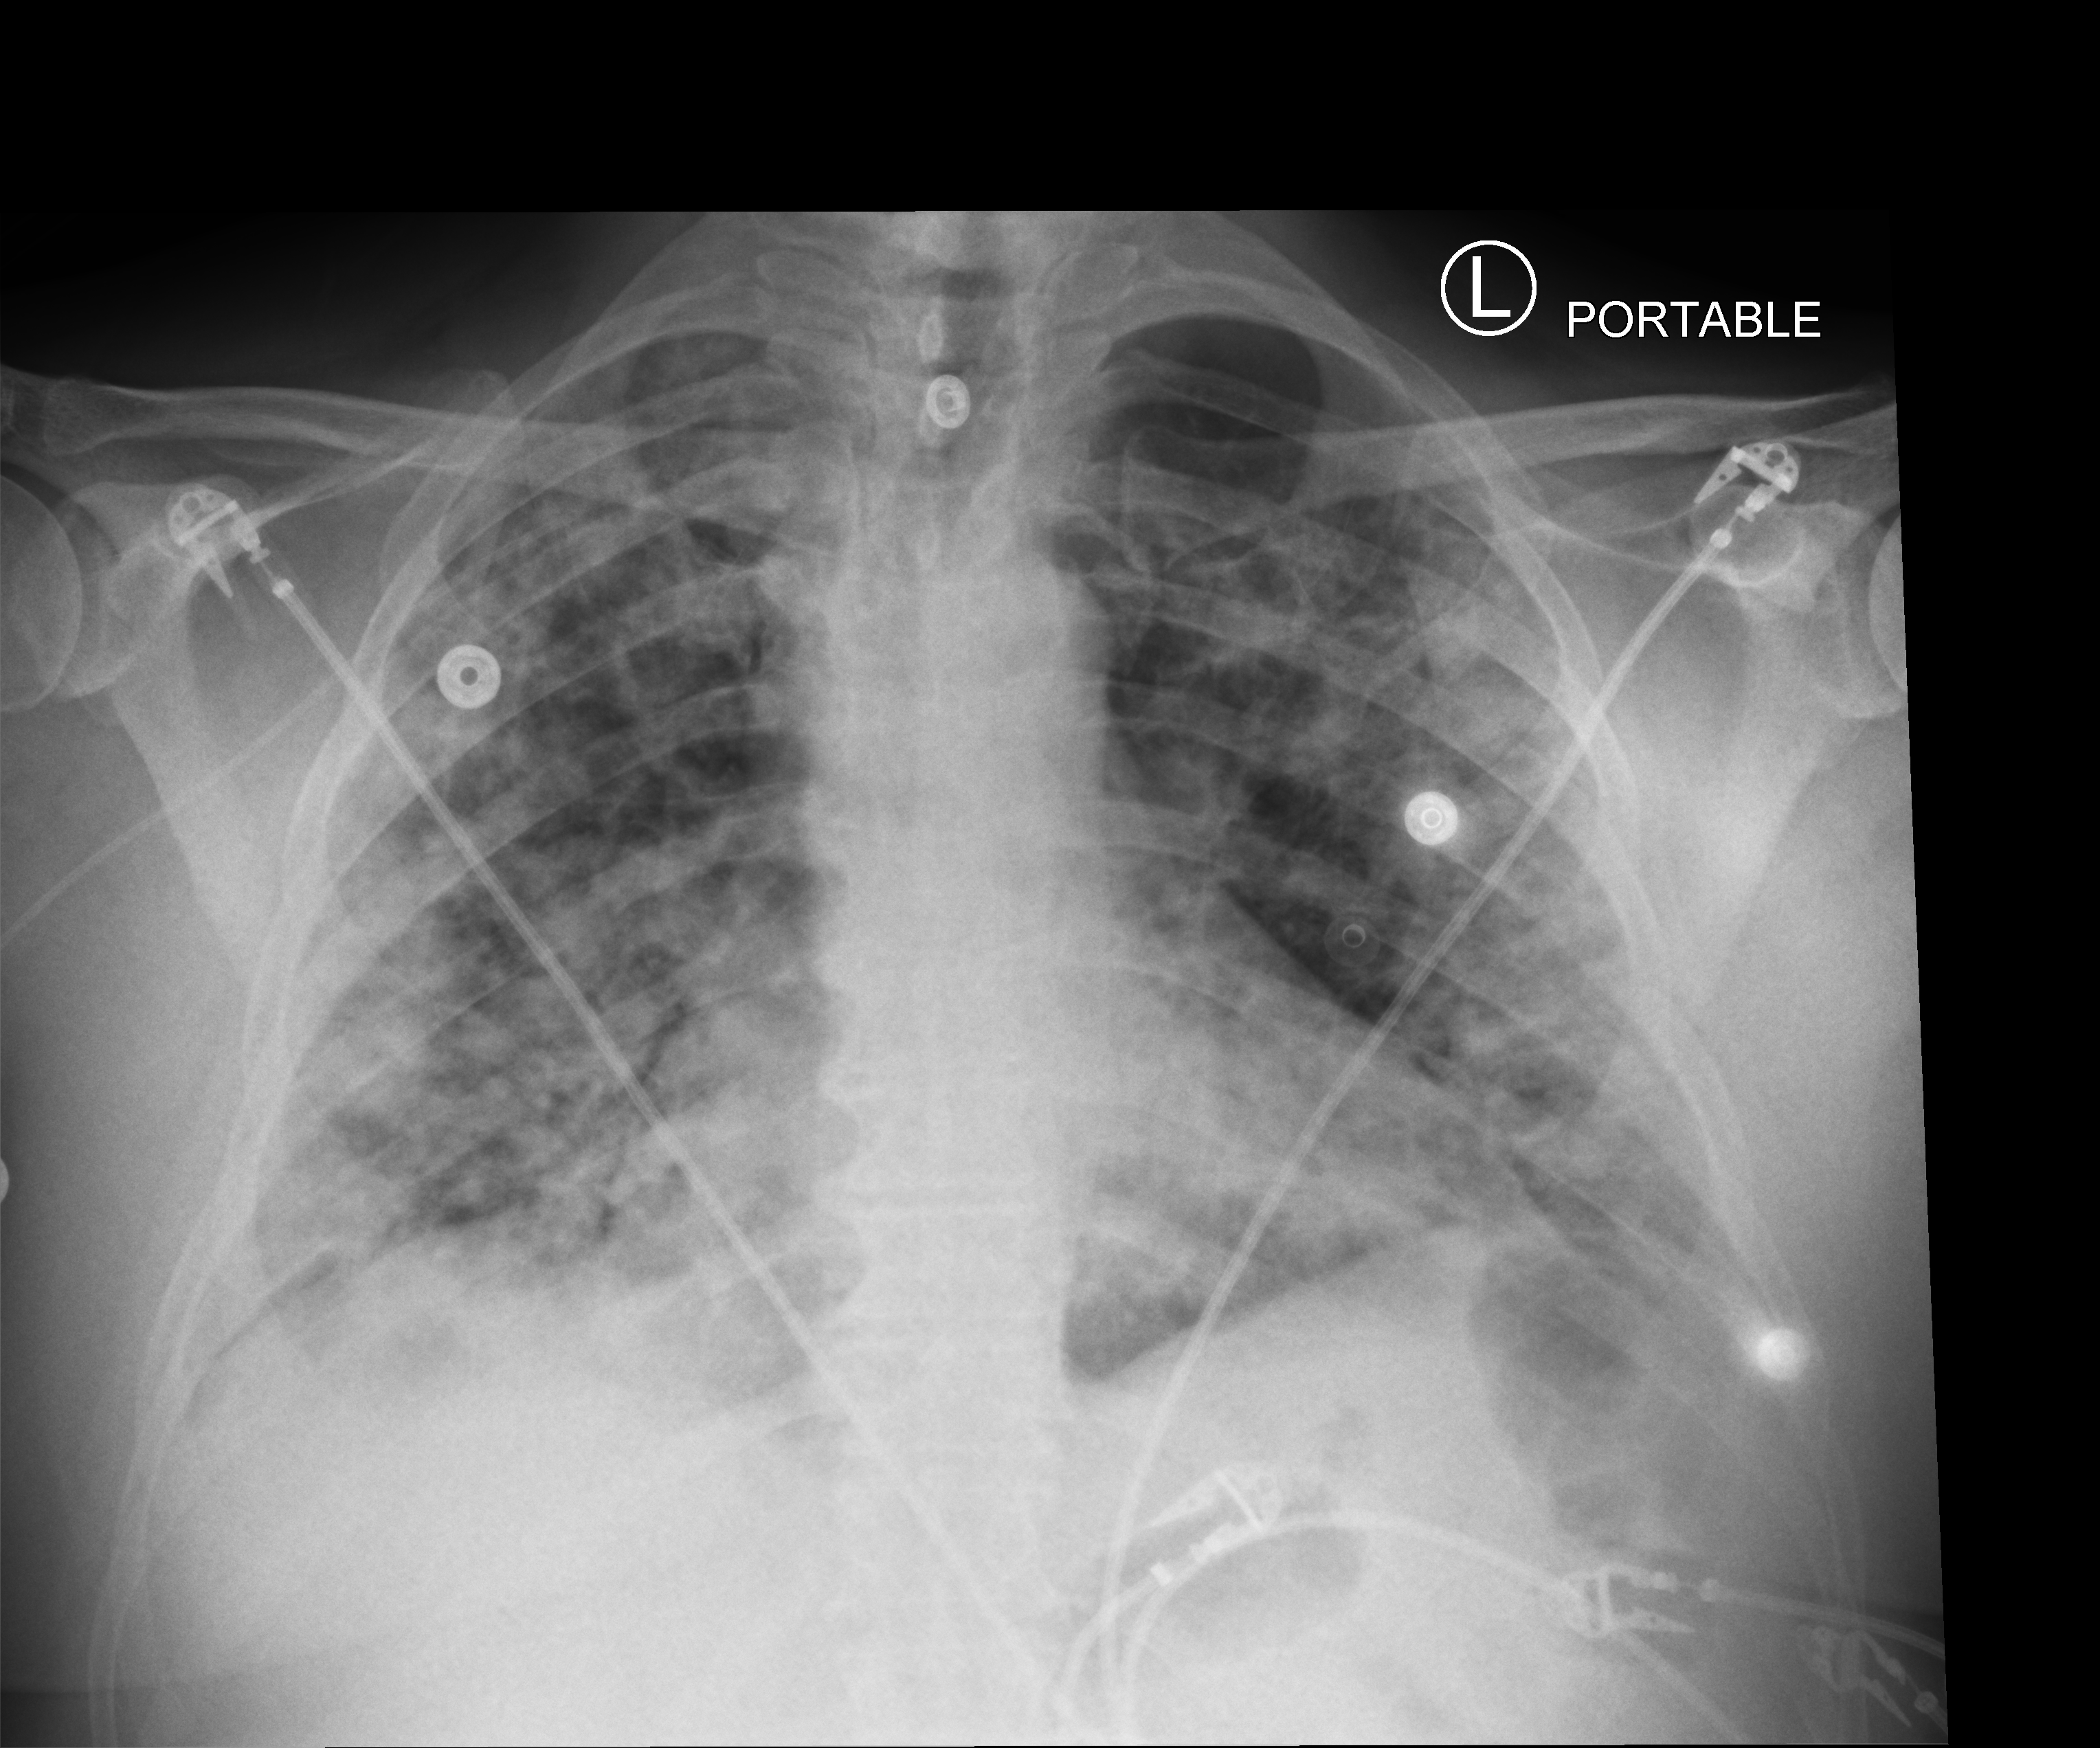
Chest X-ray (portable), anteroposterior (AP) projection. Patient hospitalised with COVID-19; male, aged 18–59 years.
From the hospital-stay record, not from the radiograph (when in the stay this image was taken is not recorded): mechanically ventilated during this hospital stay: no; admitted to intensive care during this hospital stay: yes.